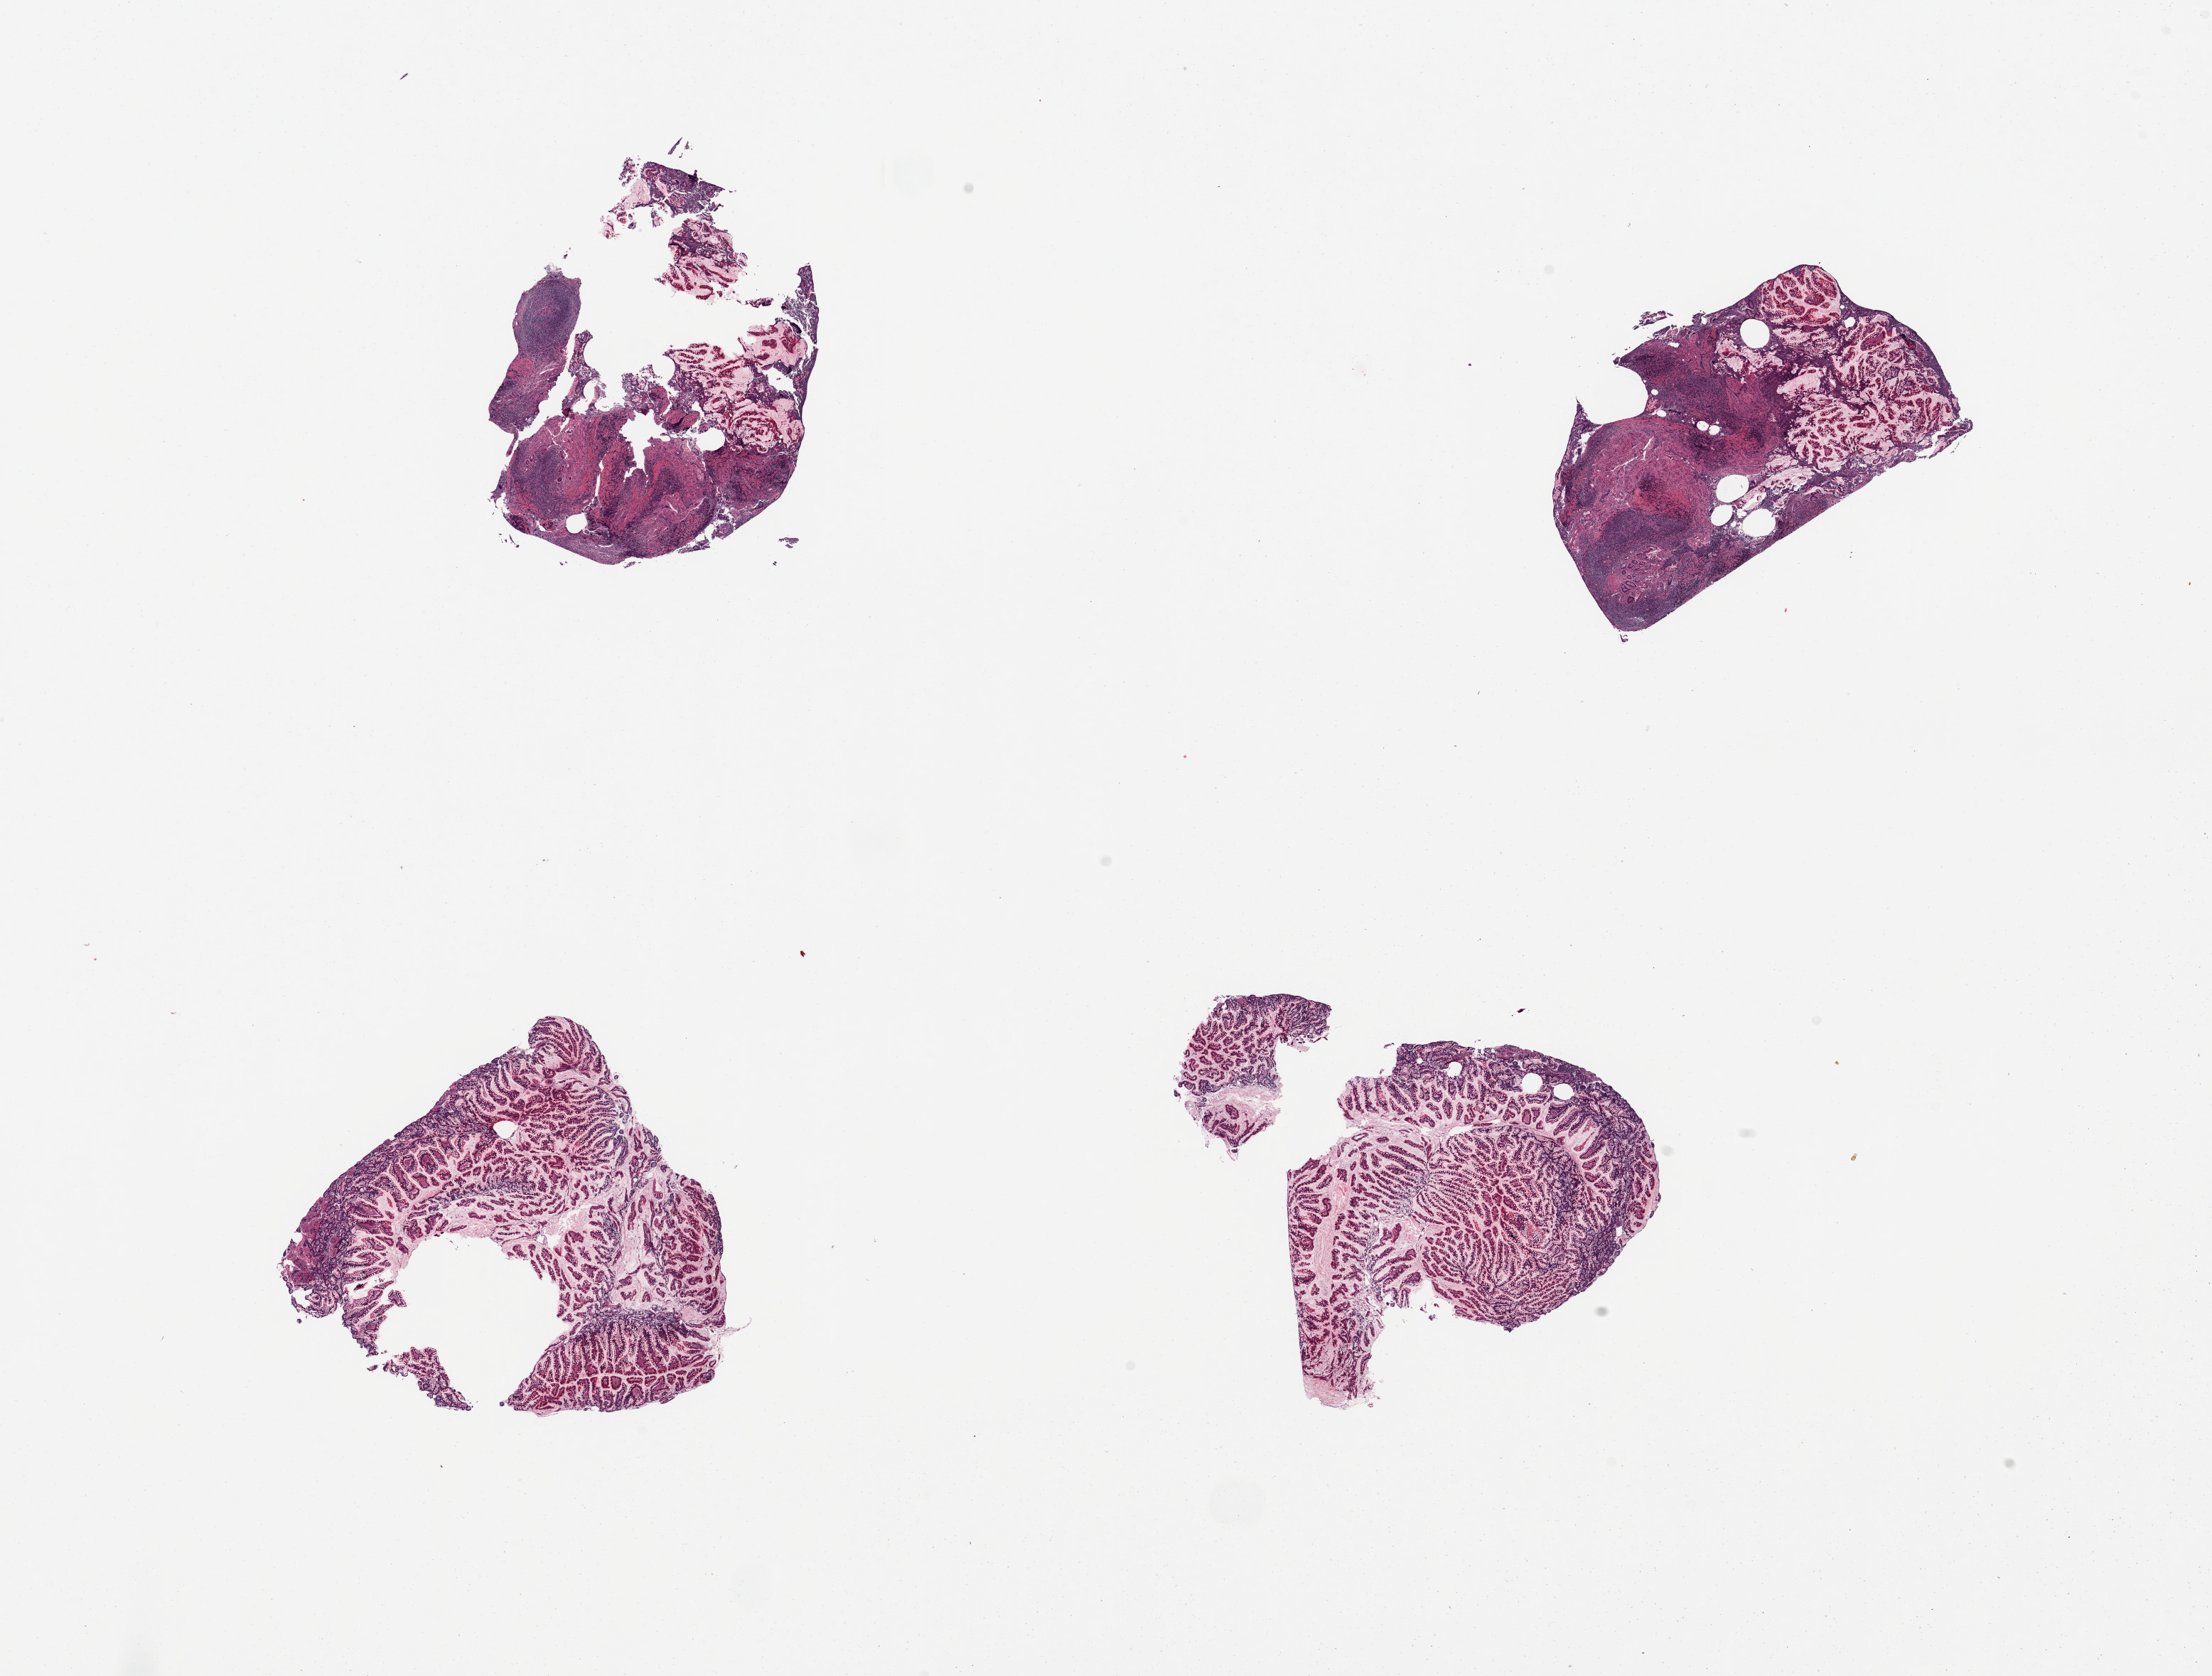
Haematoxylin and eosin whole-slide image, brightfield, shown as a low-resolution overview of the whole scanned area (about 24.6 x 18.6 mm, from a 20x scan), PAXgene-fixed, paraffin-embedded tissue, target tissue: ileum, donor tissue sample.
- pathologist's review note for this sample: 4 pieces, mainly mucosa, ~15-20% lymphoid aggregates